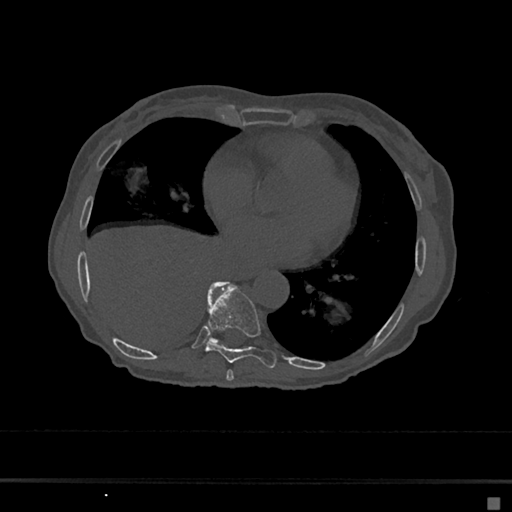
CT including the spine, one axial slice; position 317 of 797 along the scan axis; bone window (W 1800 / L 400 HU); 512 × 512 image matrix, field of view 360 × 360 mm. Patient: female, 68 years. From the clinical record (not read from this slice): primary cancer: renal.
Structures marked on this image (semi-automatically segmented with operator editing):
- T7 vertebra: bounding box (x1, y1, x2, y2) in pixels: (226, 370, 234, 381)
- T8 vertebra: (205, 282, 277, 369)
- T9 vertebra: (210, 281, 226, 343)